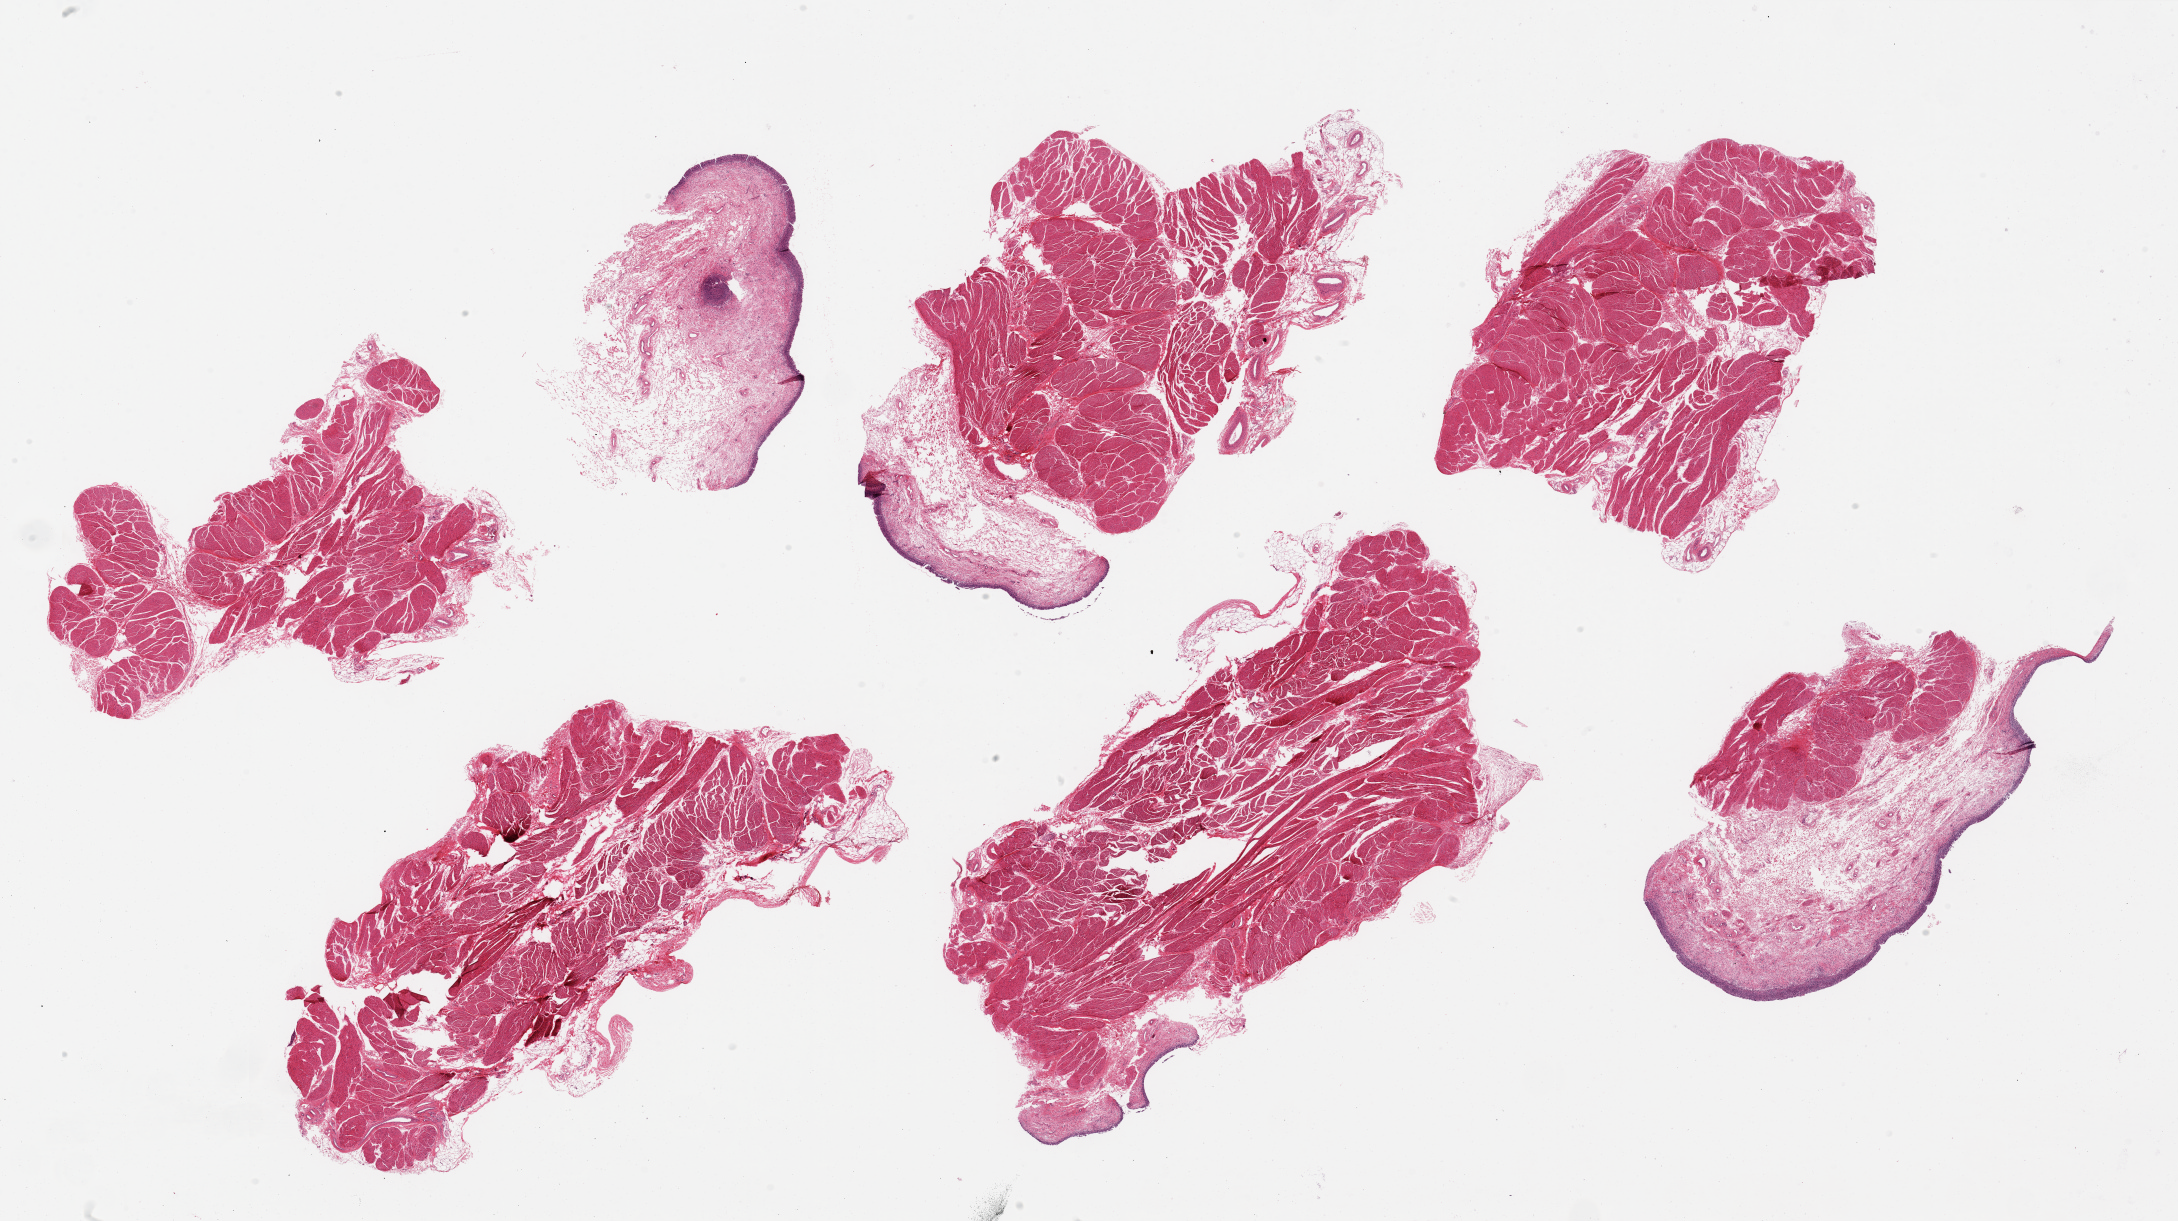
H&E whole-slide image — a low-resolution overview of the entire scanned area, about 34.5 x 19.3 mm; PAXgene-fixed paraffin-embedded (PFPE) section; target tissue: urinary bladder; tissue donor sample. Male donor.
Review note (as recorded): 5 pieces fragmented, ~8x4mm. Urothelium partly sloughed but better preserved than typical, <1% of thickness.